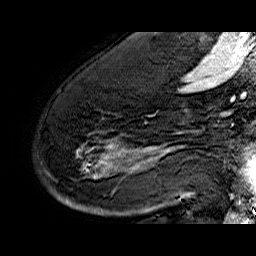
Breast MRI (dynamic contrast-enhanced), one sagittal slice; slice 41 of 60 in the series (ordered by position); dynamic contrast-enhanced series, time point 2 of 6 at this slice position (early post-contrast); 1.5 T; TE 6.4 ms, TR 32.9 ms; 4 mm slice thickness; 256 × 256 image matrix, field of view 200 × 200 mm. Female patient. From the clinical record (not read from this slice): setting: breast cancer imaged before/during neoadjuvant chemotherapy; receptor status: HR-positive, HER2-negative.
Structures marked on this image (semi-automatically segmented with operator editing):
- analysis volume of interest (the breast-tissue region the enhancement analysis was run in; not a lesion): bounding box <54,74,176,210> (left, top, right, bottom; pixels)
- tumour enhancement mask (voxels above the 100 % enhancement threshold inside the analysis volume of interest): <58,144,174,203>